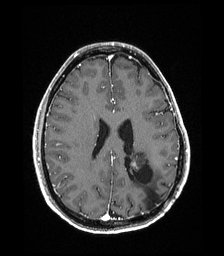
Brain MRI from a brain-tumour surgery series, one axial slice. Slice 77 of 192 in the series (ordered by position). T1-weighted post-contrast. 1 mm slice thickness. 224 × 256 image matrix, field of view 224 × 256 mm. From the clinical record (not read from this slice): histopathology: Low grade glioma; IDH mutation: no; tumour location: Left Parieto-Occipital Intraventricular.
Annotated regions visible in this slice (expert manual segmentation):
- previous resection cavity: bounding box [x1, y1, x2, y2] px = [129, 164, 162, 208]
- tumour: [129, 152, 148, 171]